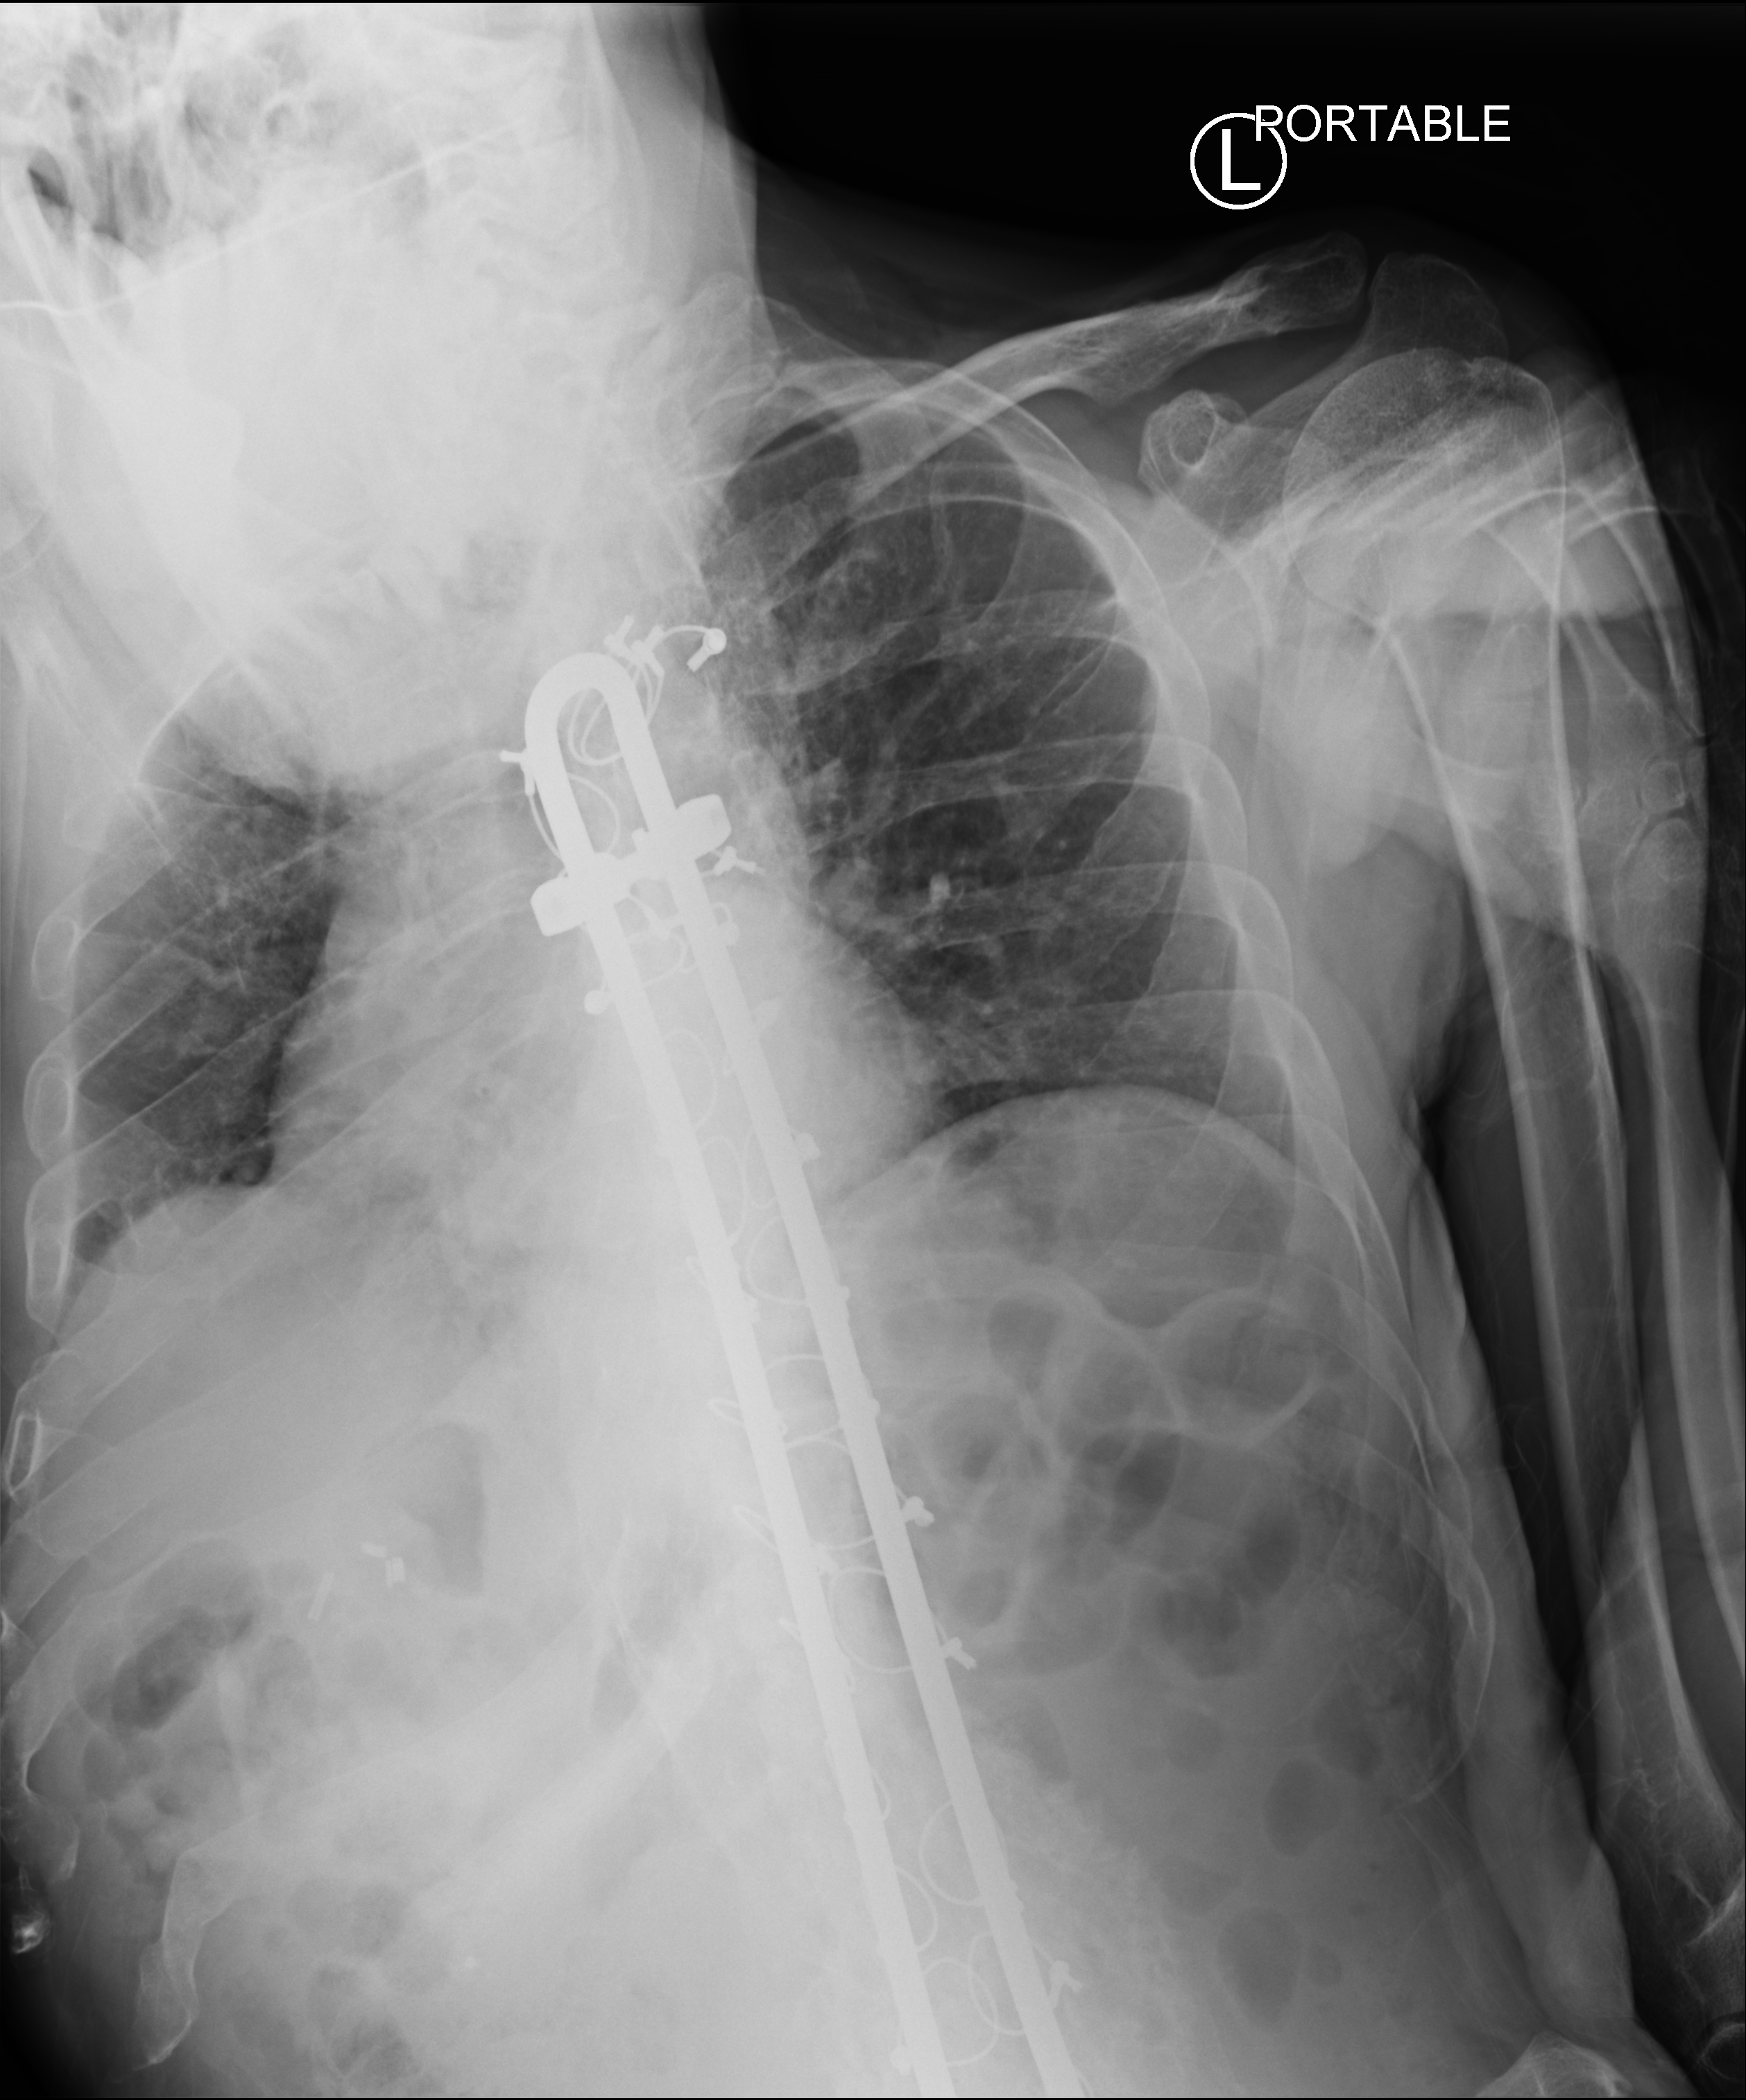
Chest X-ray (portable), anteroposterior (AP) projection. Patient hospitalised with COVID-19; male, aged 60–74 years.
From the hospital-stay record, not from the radiograph (when in the stay this image was taken is not recorded): admitted to intensive care during this hospital stay: no; mechanically ventilated during this hospital stay: no; length of hospital stay: 7 days.